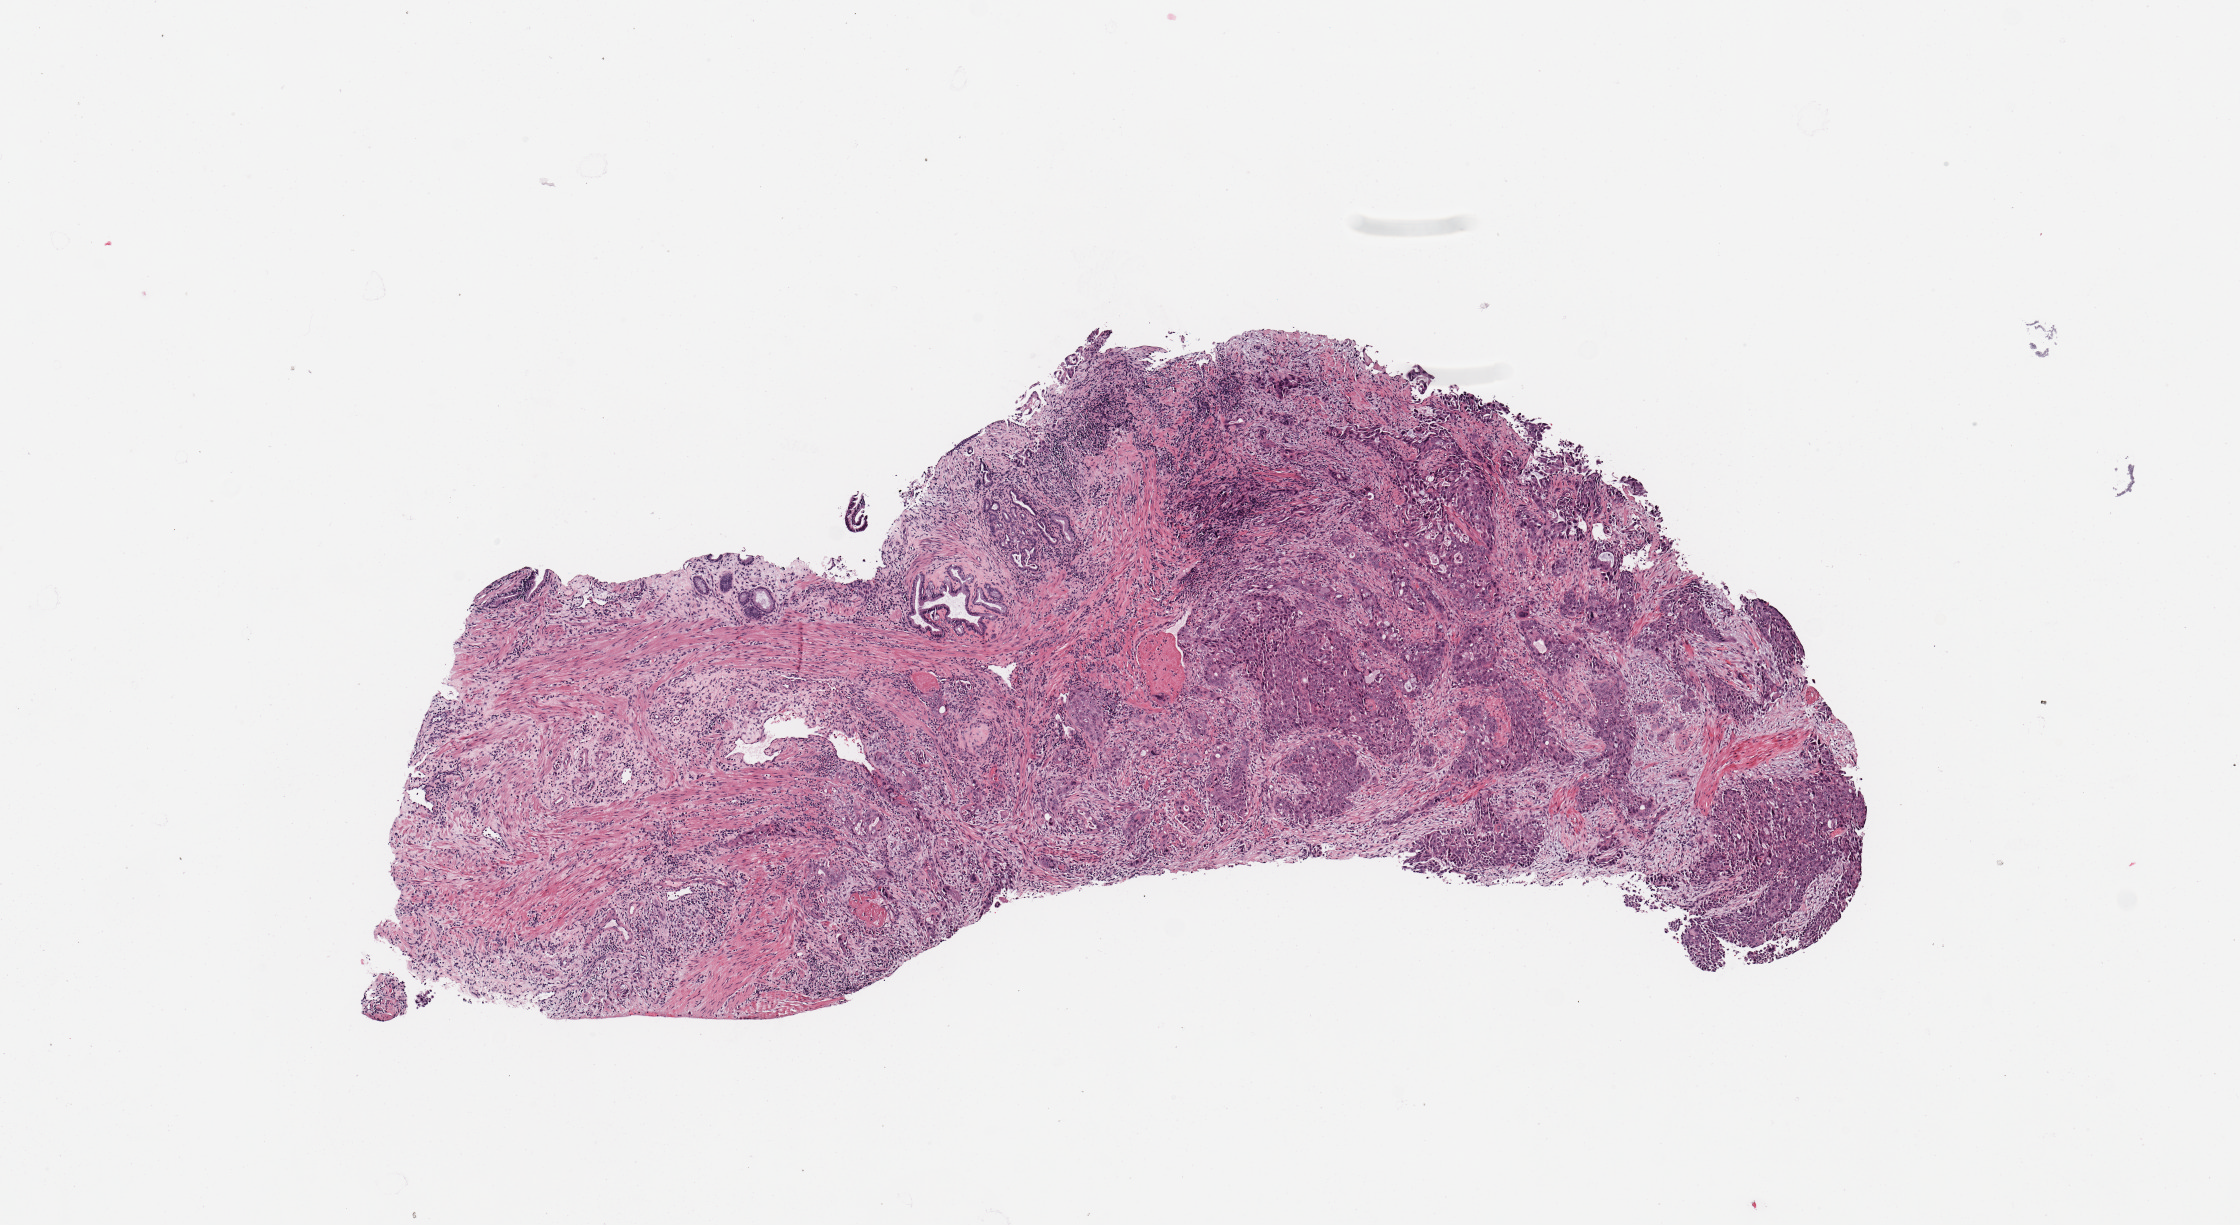
Whole-slide histology image, H&E-stained, whole scanned area (about 8.9 x 4.8 mm) shown as a low-resolution overview; tumour tissue sample, sampled site: pancreas. 55-year-old male patient. Composition of this section per pathologist review: tumour nuclei 30%, necrosis 0%.
Histologic diagnosis: Infiltrating duct carcinoma, NOS.